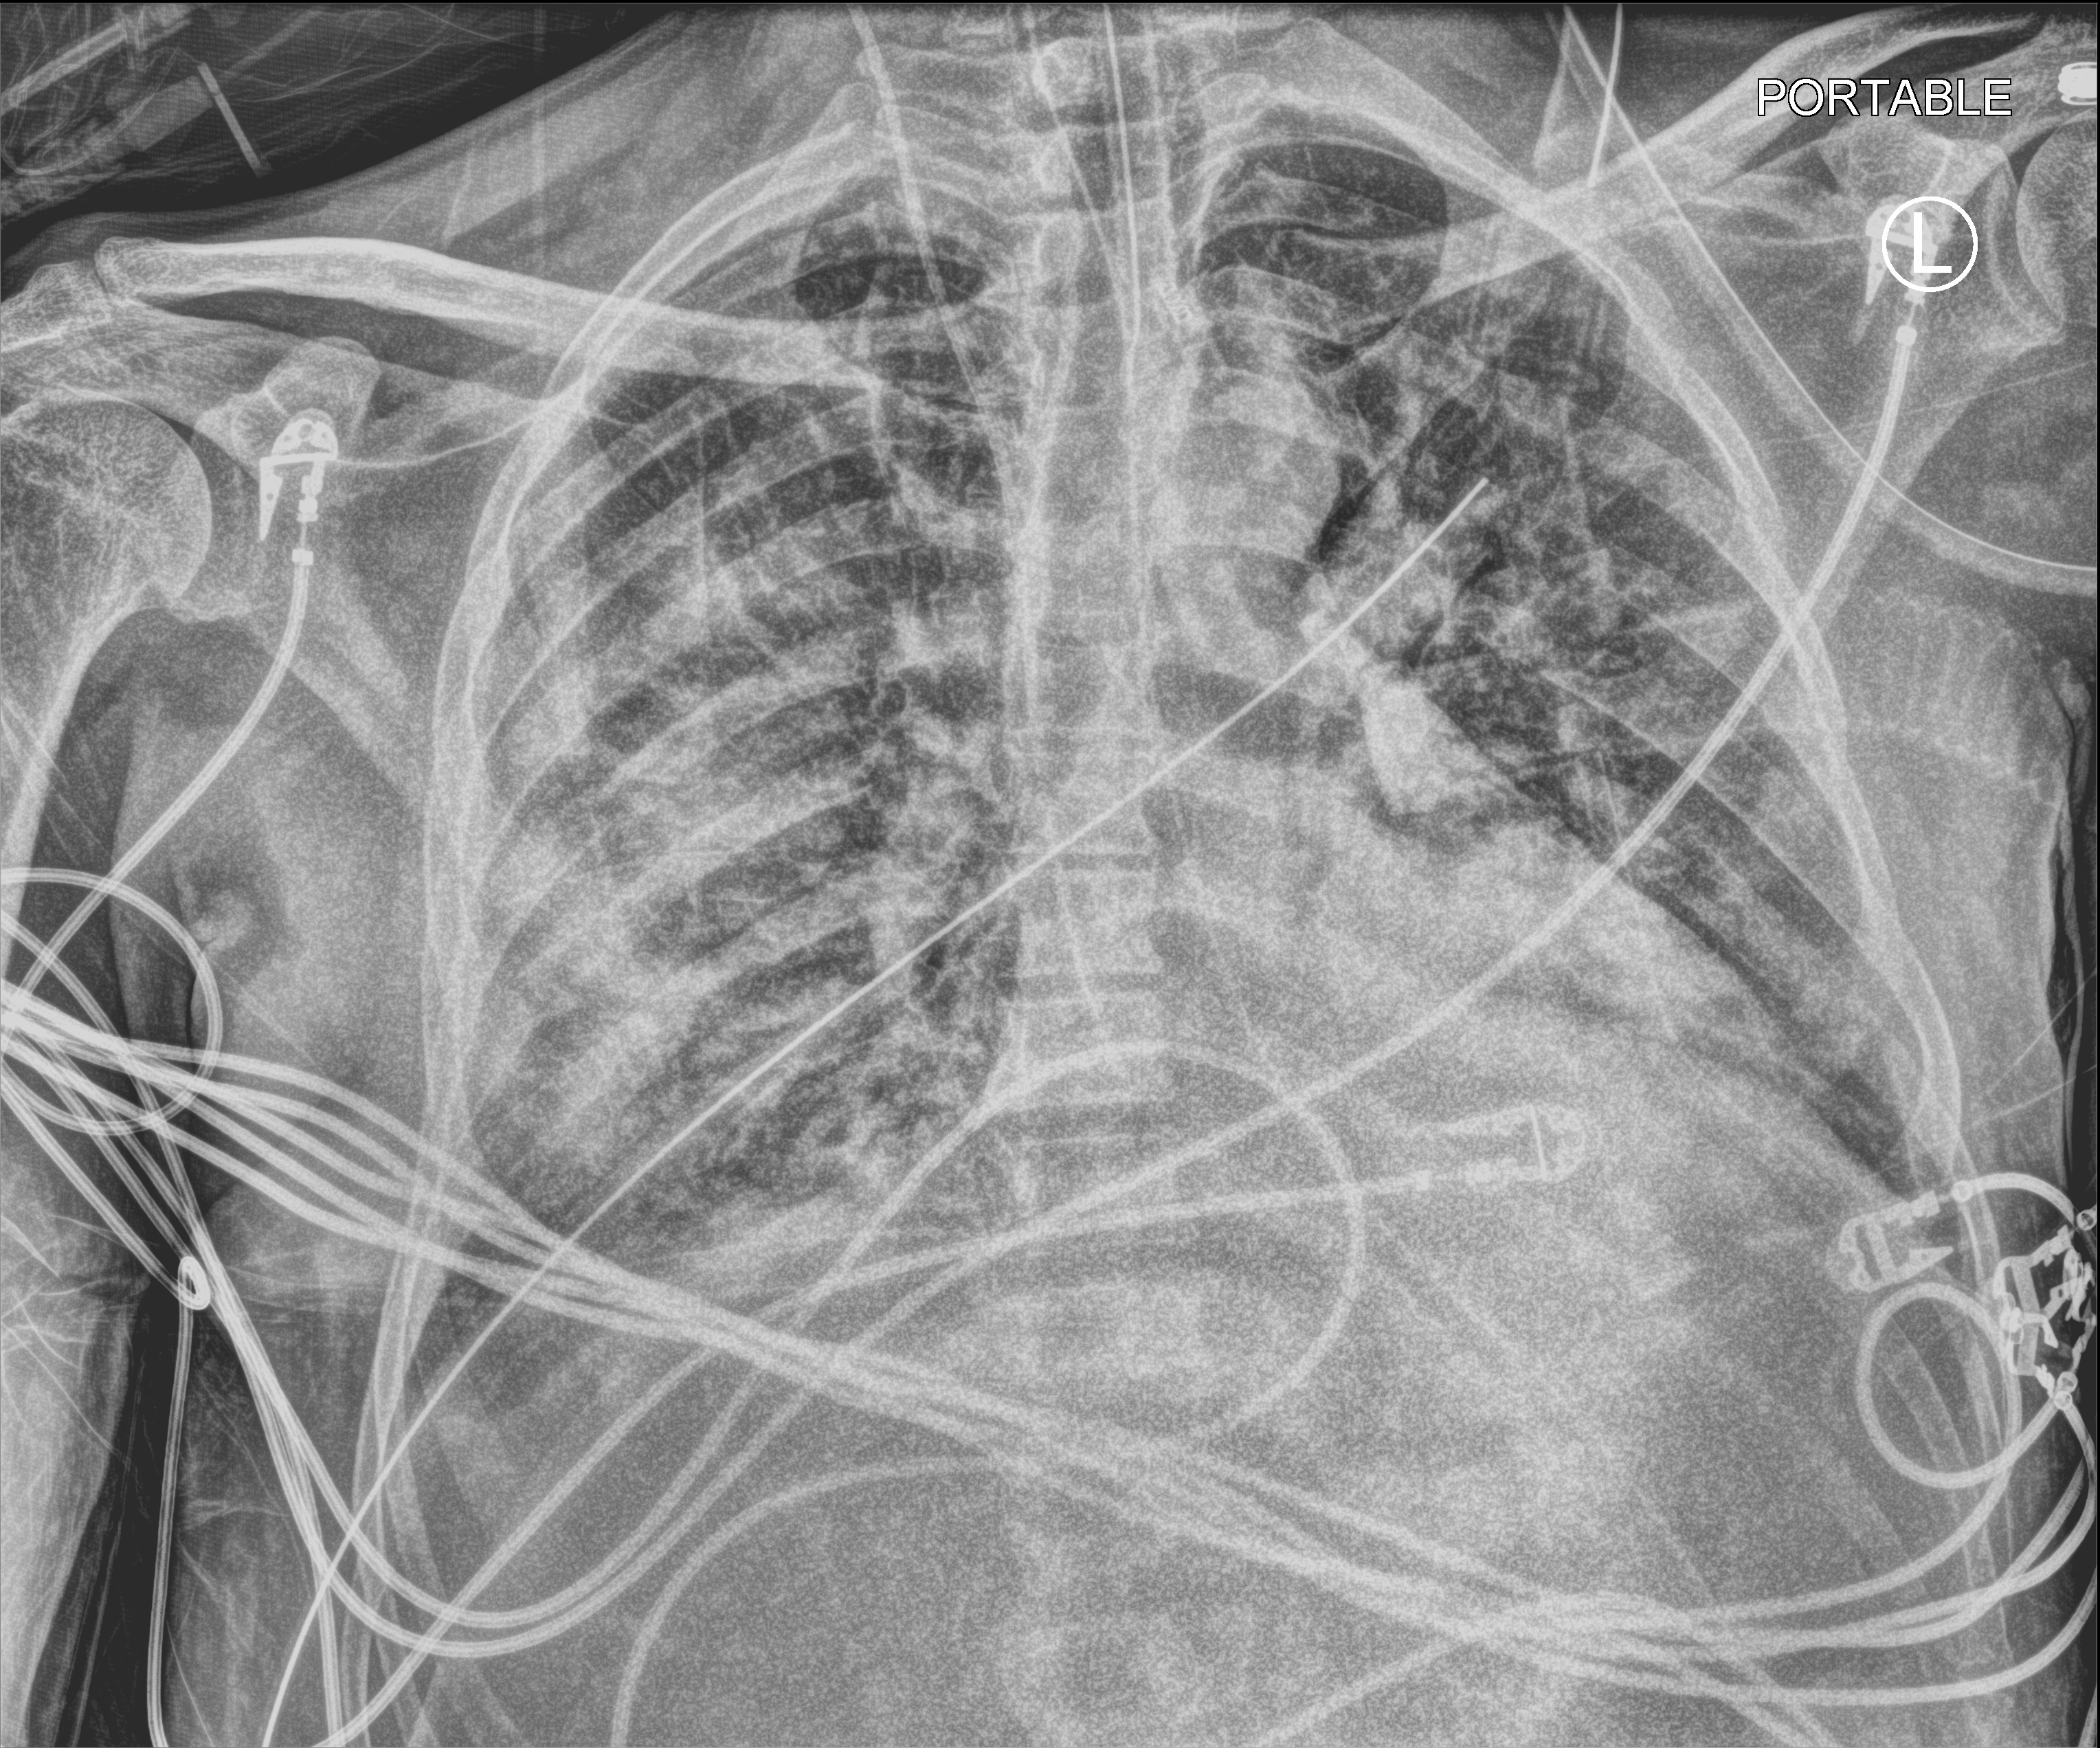
Chest X-ray (portable). Male patient hospitalised with COVID-19, age 18–59 years.
Hospital-stay facts (about this admission, not read from this image; timing relative to this image not recorded):
- admitted to intensive care during this hospital stay: yes
- other chronic lung disease (admission record): no